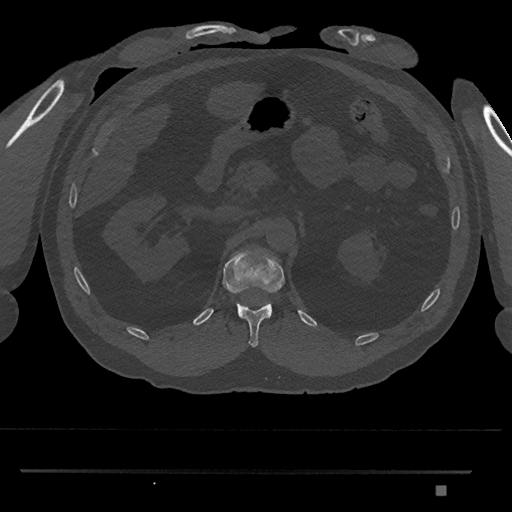
CT including the spine, one axial slice. Position 872 of 1134 along the scan axis. Reconstruction kernel Br40s/3. Bone window (W 1800 / L 400 HU). 512 × 512 image matrix, field of view 429 × 429 mm. Male patient, age 65 years. From the clinical record (not read from this slice): primary cancer: prostate.
Annotated regions visible in this slice (semi-automatically segmented with operator editing):
- T12 vertebra: bounding box [x1, y1, x2, y2] px = [222, 252, 285, 347]